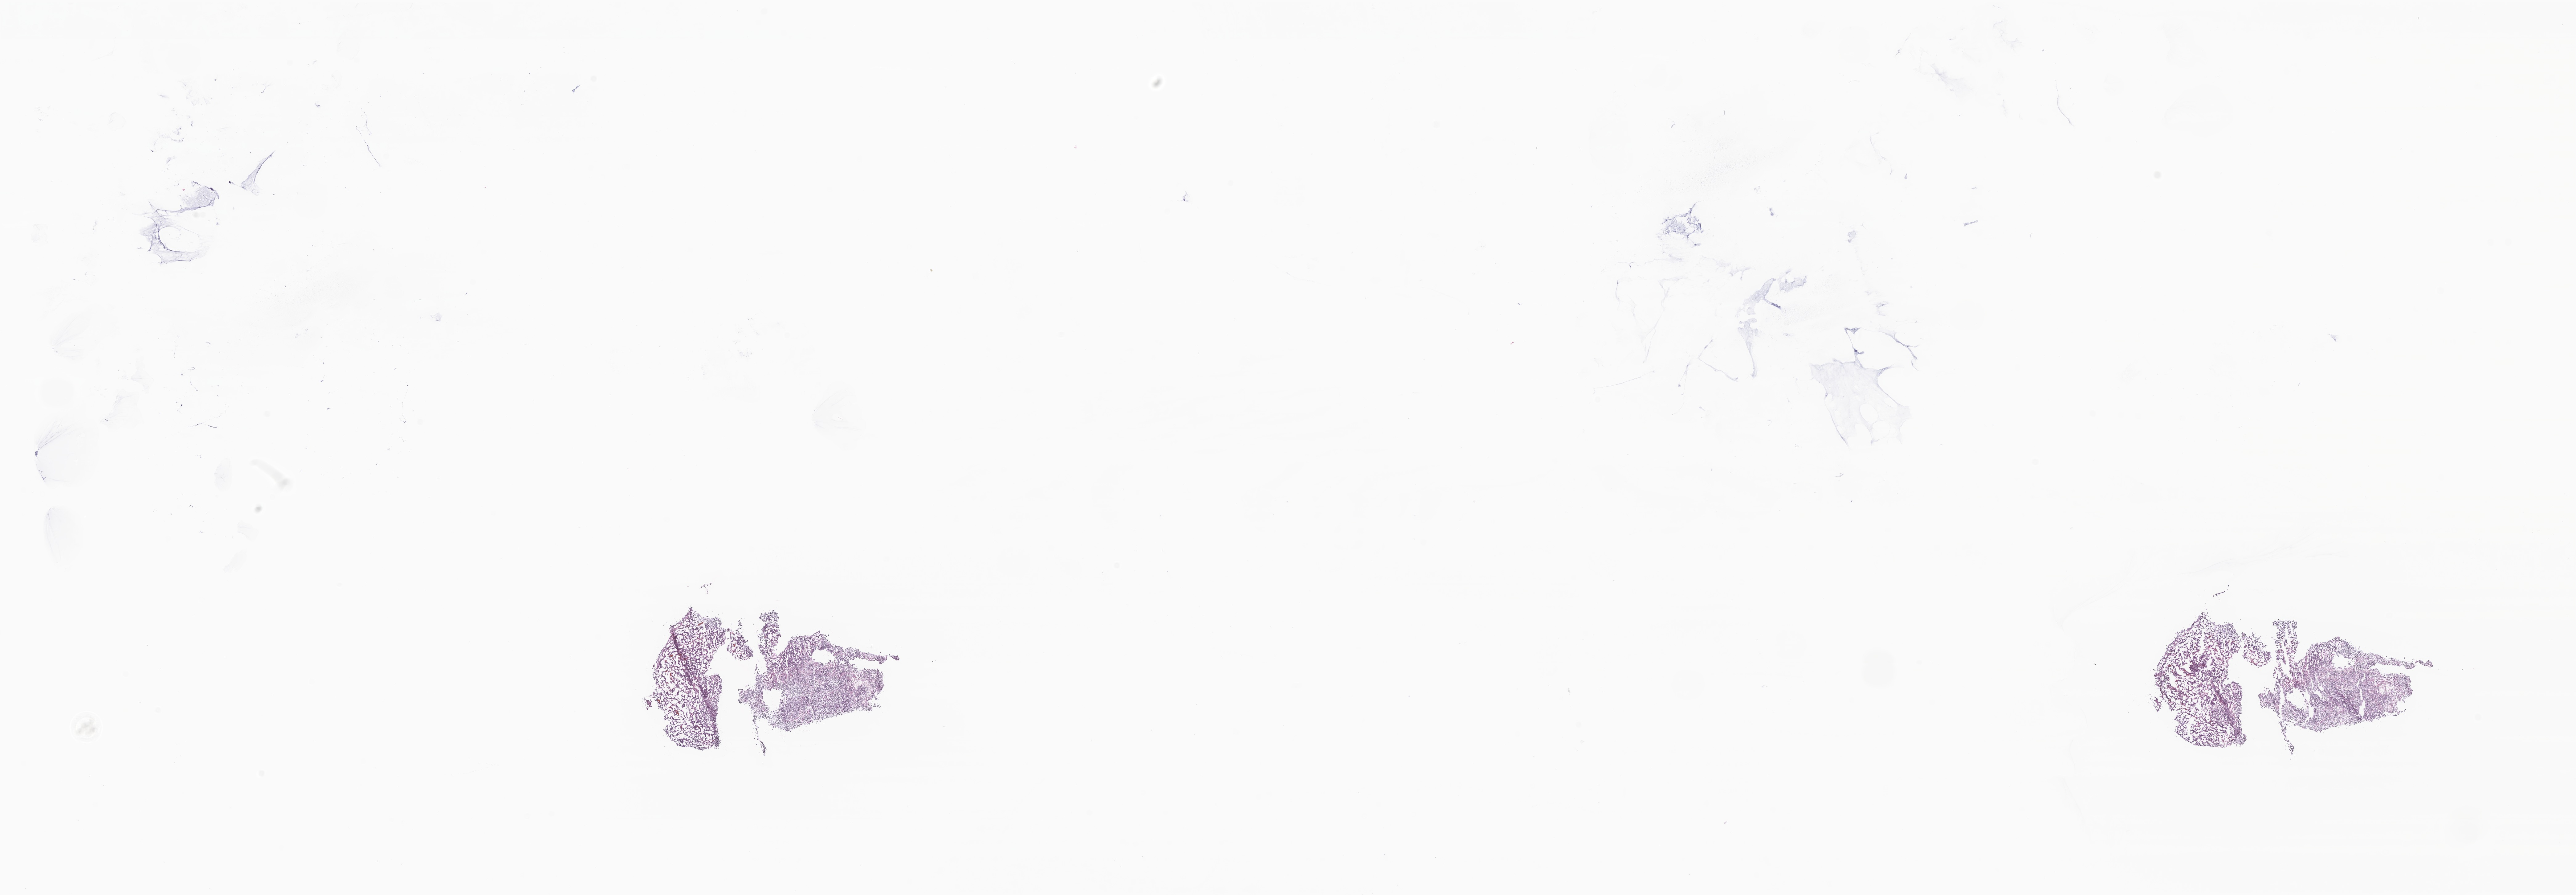
Hematoxylin and eosin (H&E) whole-slide image of tumor tissue from the brain, low-resolution overview of the scanned area, about 35.2 x 12.2 mm, frozen section. Patient: male, age 480 days (about 1.3 years).
Diagnosis (ICD-O-3 morphology term): Medulloblastoma, NOS.